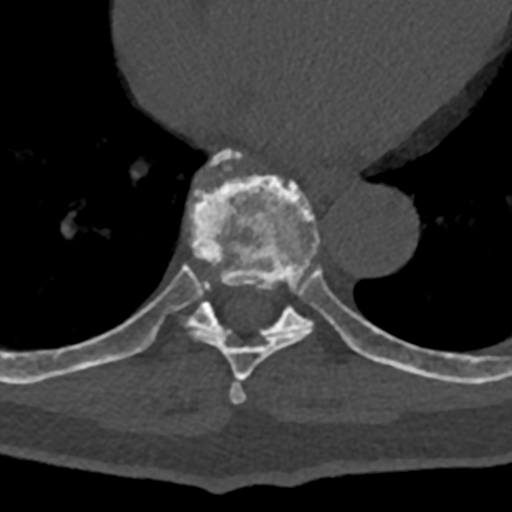
CT including the spine, one axial slice; position 687 of 797 along the scan axis; 120 kVp; bone window (W 1800 / L 400 HU); 0.5 mm slice thickness; 512 × 512 image matrix, field of view 160 × 160 mm. Male patient, age 74 years. From the clinical record (not read from this slice): primary cancer: renal; vertebrae with lytic lesions (as recorded): T10, L1, L2, L3, L4, L5.
Outlined on this slice (semi-automatically segmented with operator editing):
- T7 vertebra: bounding box <229,378,247,404> (left, top, right, bottom; pixels)
- T8 vertebra: <70,153,380,380>
- T9 vertebra: <105,149,432,378>